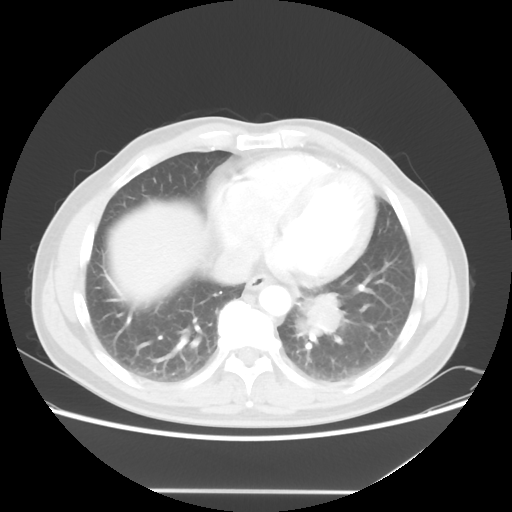
Chest CT, one axial slice; position 20 of 56 along the scan axis; reconstruction kernel STANDARD; 120 kVp; lung window (W 1500 / L -600 HU); 5 mm slice thickness; 512 × 512 image matrix. Patient: male, 61 years. Case-level facts recorded for this patient, not image findings: clinical TNM (as recorded): T1c N0 M0.
Annotated regions visible in this slice (bounding box drawn by a radiologist):
- lung tumour (recorded histology: adenocarcinoma): bounding box [x1, y1, x2, y2] px = [289, 286, 346, 348]